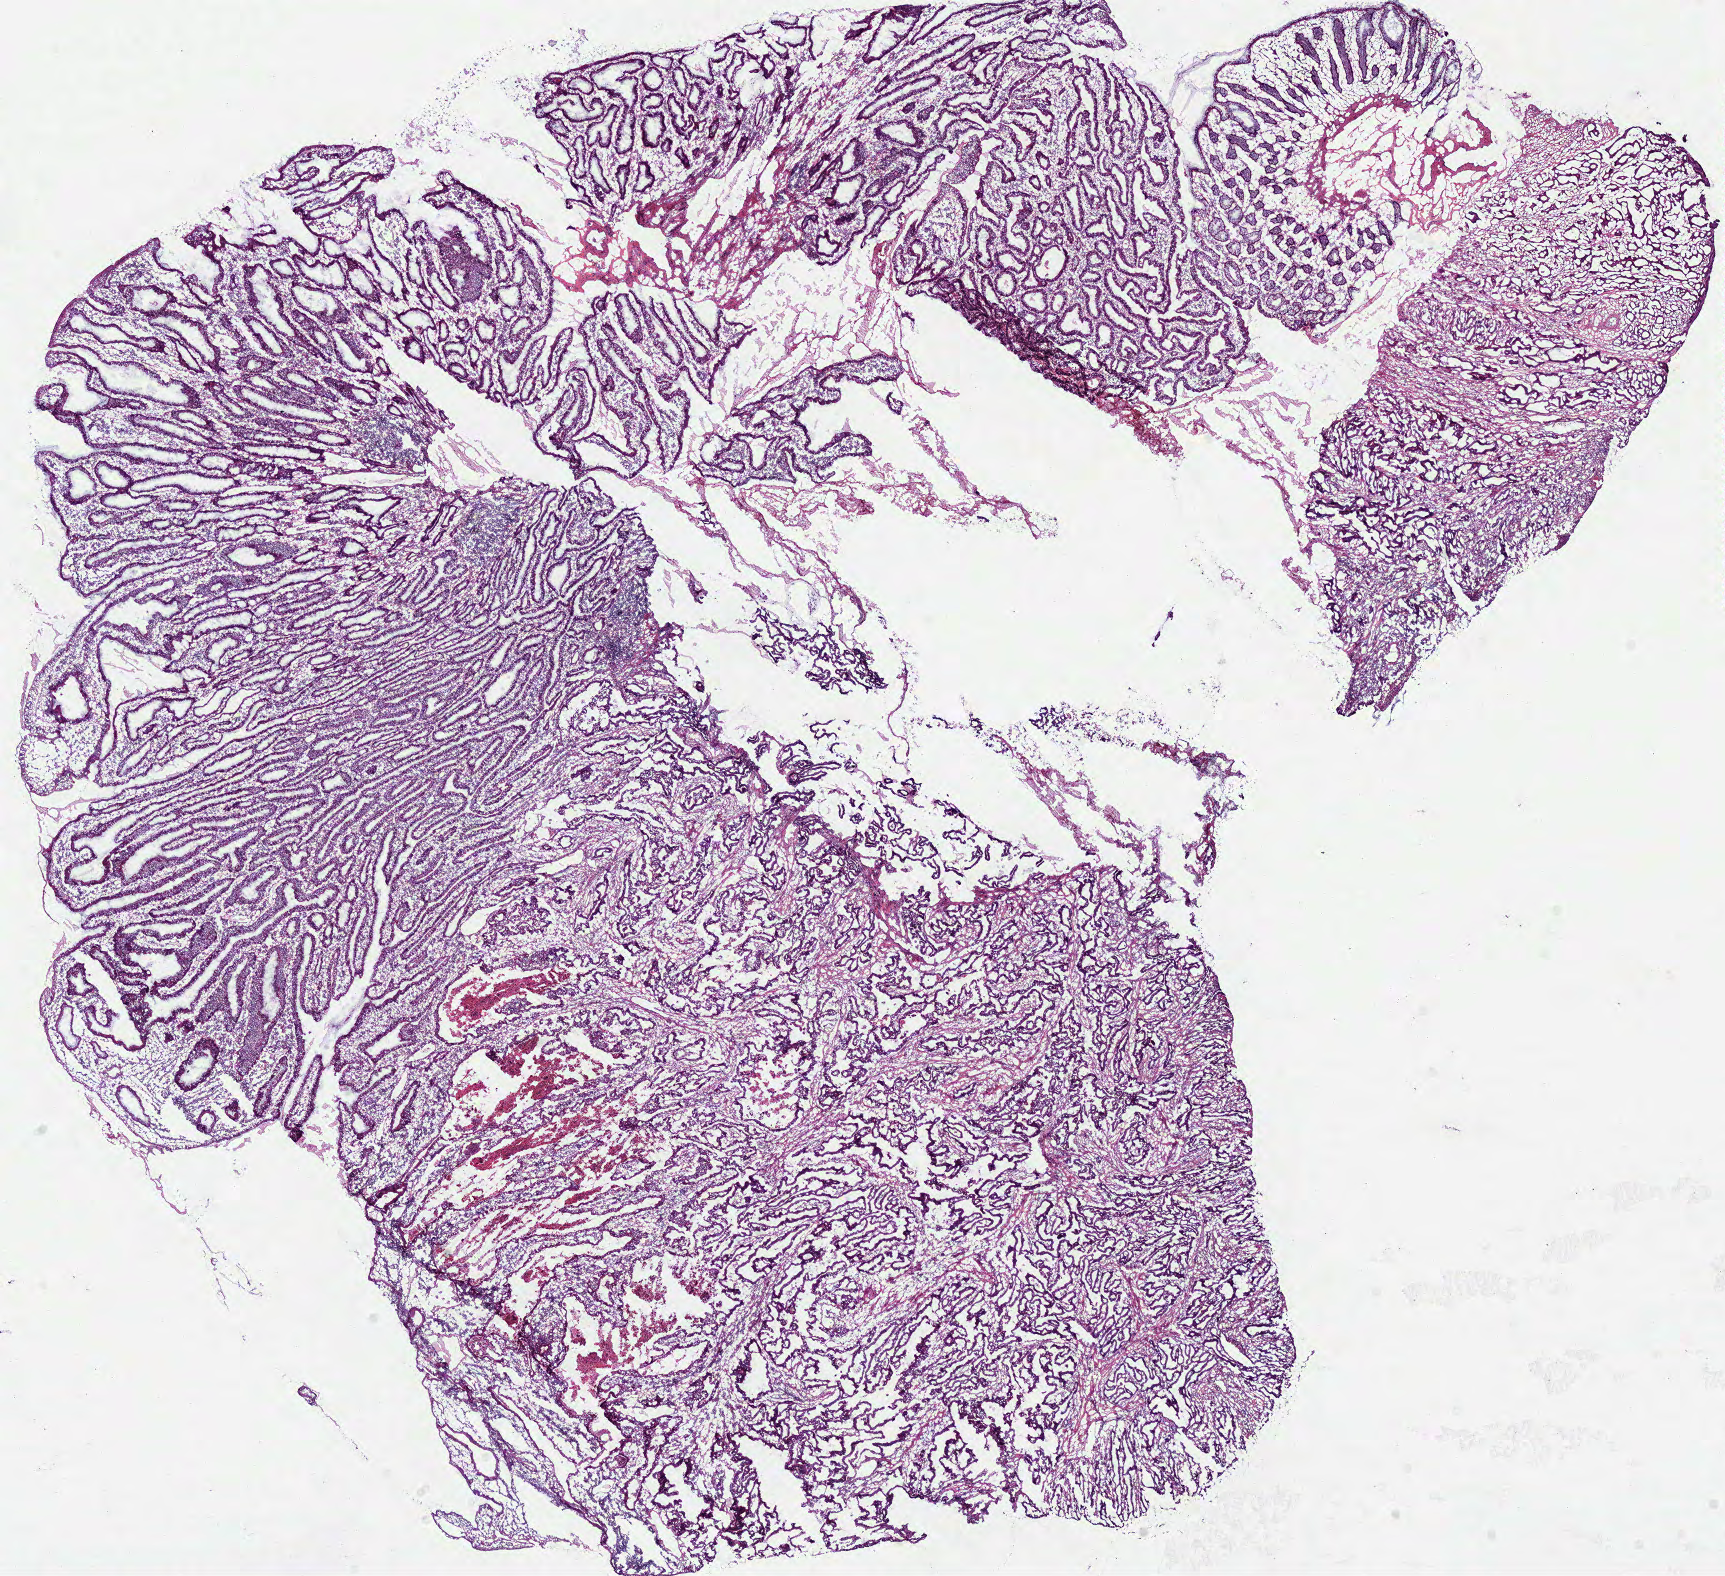
Digitized H&E-stained tissue section (whole slide) — low-resolution overview of the scanned area, about 13.6 x 12.4 mm; frozen section from the top of the tissue portion; primary tumour sample from the colon. Female, age 59 years at initial diagnosis. Slide review estimates, as recorded: tumour cells 77%, tumour nuclei 80%, normal cells 5%, stromal cells 10%, necrosis 8%.
AJCC pathologic stage: I (7th edition). Pathologic diagnosis: Adenocarcinoma, NOS (sigmoid colon). Lymph nodes positive (case pathology): 0 of 5 examined.